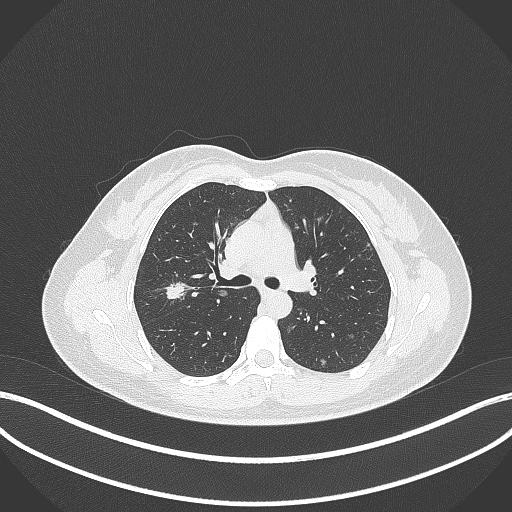
Chest CT, one axial slice. Position 216 of 307 along the scan axis. Reconstruction kernel B70f. 120 kVp. Lung window (W 1500 / L -600 HU). 1 mm slice thickness. 512 × 512 image matrix. Patient: female, 33 years. Case-level facts recorded for this patient, not image findings: clinical TNM (as recorded): T1c N0 M0; histopathological grade: G2-G3.
Outlined on this slice (rectangle marked by the reading radiologist):
- lung tumour (recorded histology: adenocarcinoma): bounding box <162,278,191,303> (left, top, right, bottom; pixels)